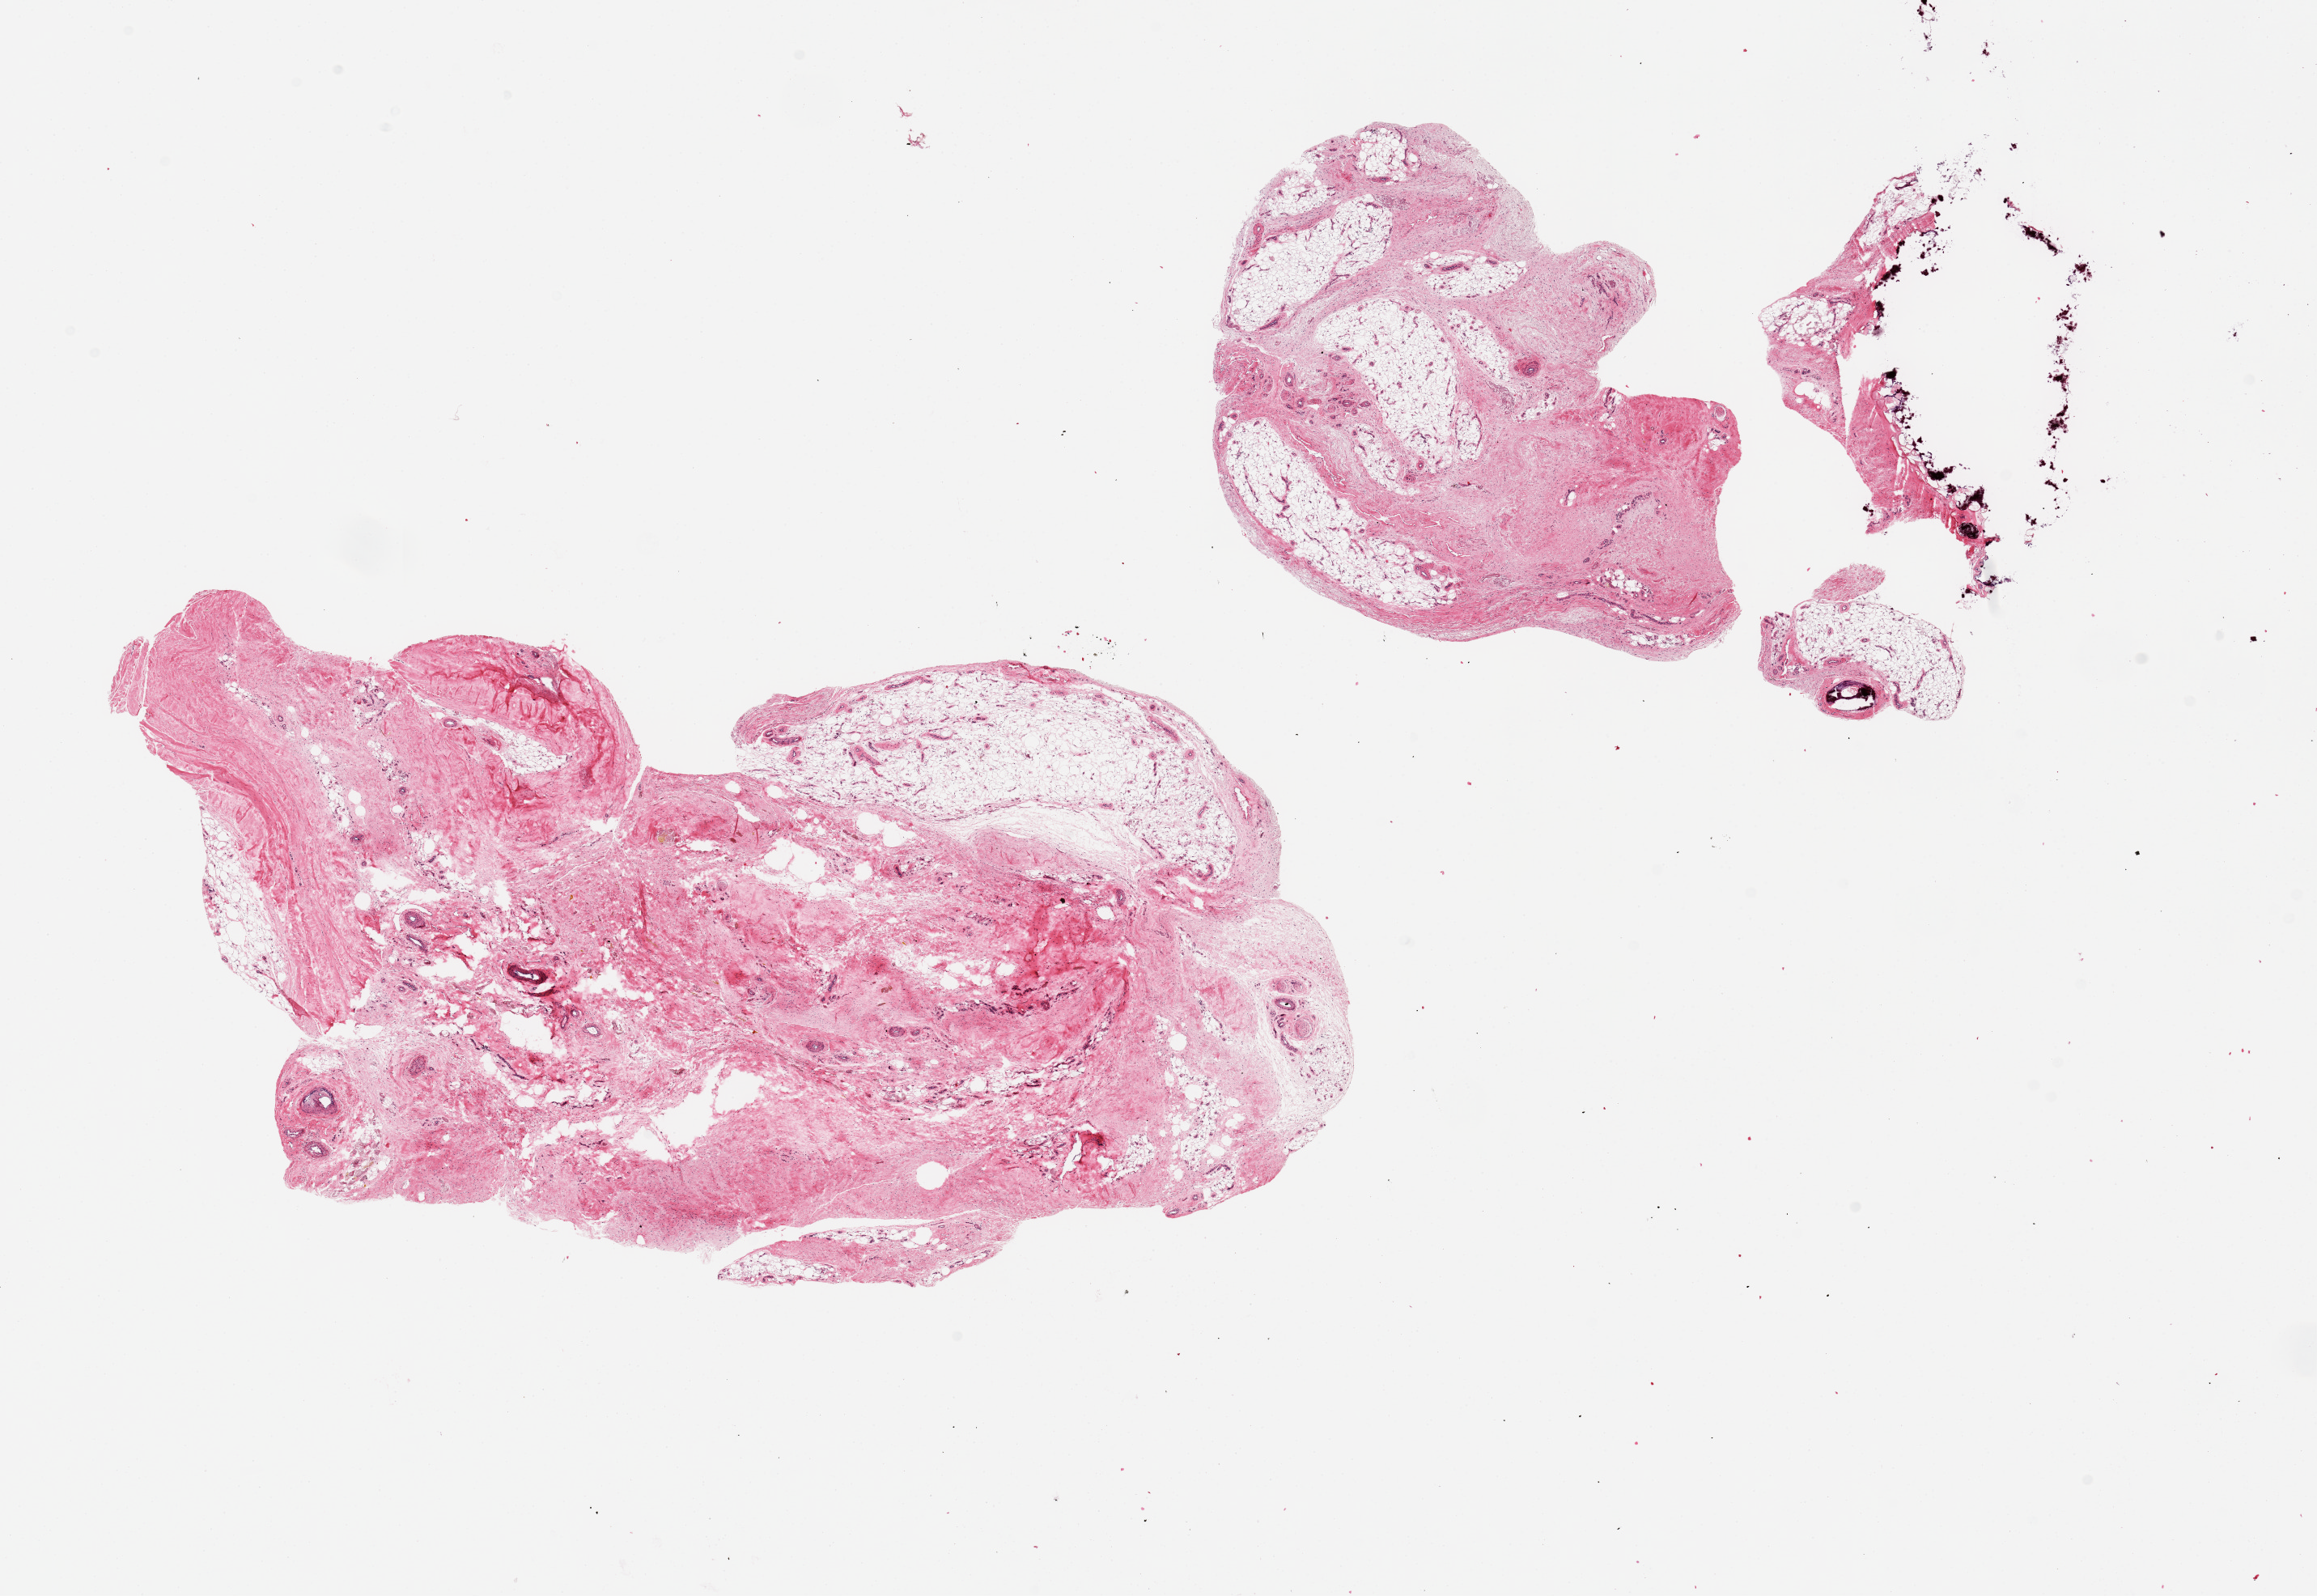
Digitized H&E-stained section — shown as a low-resolution overview of the whole scanned area (about 22.6 x 15.6 mm, slide scanned at 20x), PAXgene-fixed paraffin-embedded (PFPE) section, target tissue: adipose tissue, donor tissue sample. Donor sex: female.
Pathologist's review note for this sample: 2 pieces prominent fibrosis surrounds islets of uninvovled adipose tissue, ~50% of specimen.